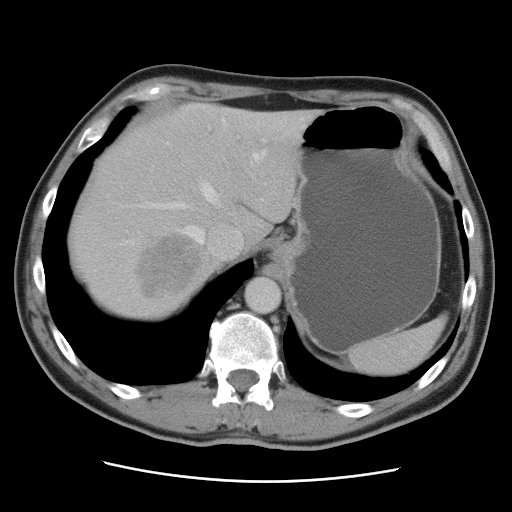
Contrast-enhanced abdominal CT, one axial slice. Position 71 of 89 along the scan axis. Intravenous contrast given. Soft-tissue window (W 400 / L 40 HU). 512 × 512 image matrix, field of view 366 × 366 mm. Male patient, age 59 years. Case-level facts recorded for this patient, not image findings: diagnosis: colorectal cancer liver metastases, imaged before liver resection; multiple liver metastases: yes; largest metastasis: 0.6 cm; disease in both lobes: yes.
Annotated regions visible in this slice (expert manual segmentation):
- hepatic veins: bounding box <143,119,303,255> (left, top, right, bottom; pixels)
- liver: <66,104,318,322>
- planned liver remnant (the part of the liver to remain after resection): <115,104,319,244>
- portal vein (with intrahepatic branches): <263,139,266,142>
- liver metastasis: <139,236,201,297>